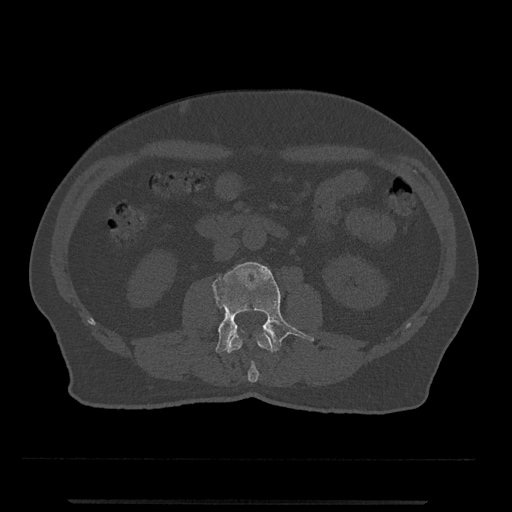
CT including the spine, one axial slice; slice 221 of 797 in the series (ordered by position); 120 kVp; bone window (W 1800 / L 400 HU); 0.5 mm slice thickness; 512 × 512 image matrix, field of view 419 × 419 mm. Male patient, age 63 years. Case-level facts recorded for this patient, not image findings: primary cancer: prostate.
Annotated regions visible in this slice (semi-automatically segmented with operator editing):
- L2 vertebra: bounding box (x1, y1, x2, y2) in pixels: (227, 332, 273, 383)
- L3 vertebra: (212, 262, 314, 353)